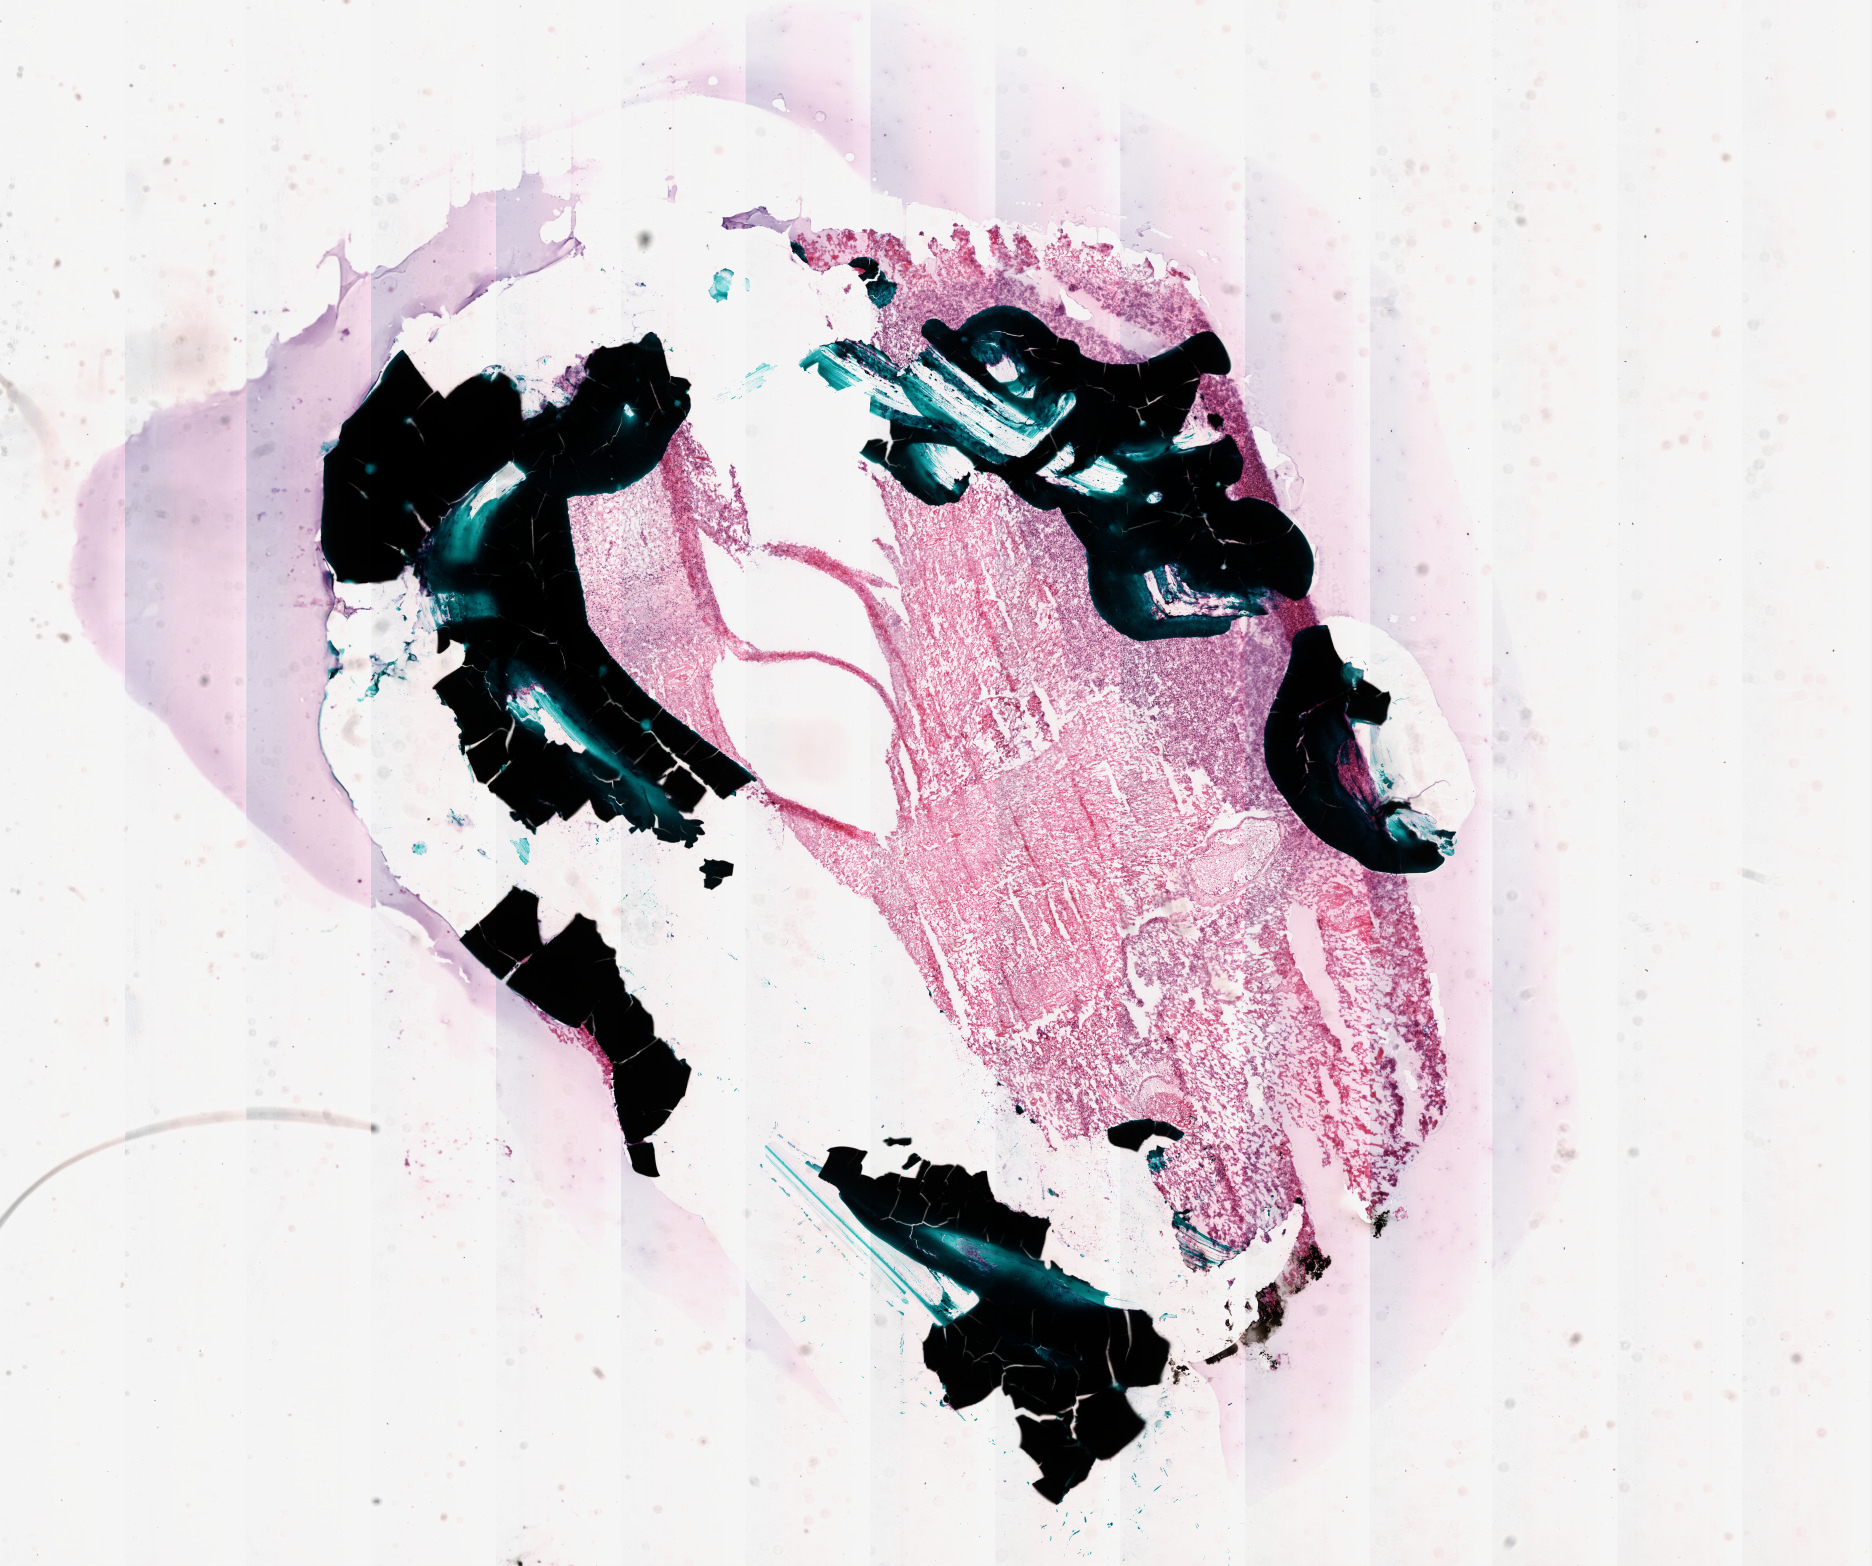
Whole-slide histology image, H&E — a low-resolution overview of the entire scanned area, about 15.0 x 12.5 mm (acquisition: 20x scan); frozen section; brain, primary tumour sample. Female, age 63 years at initial diagnosis.
Histologic diagnosis: Glioblastoma.